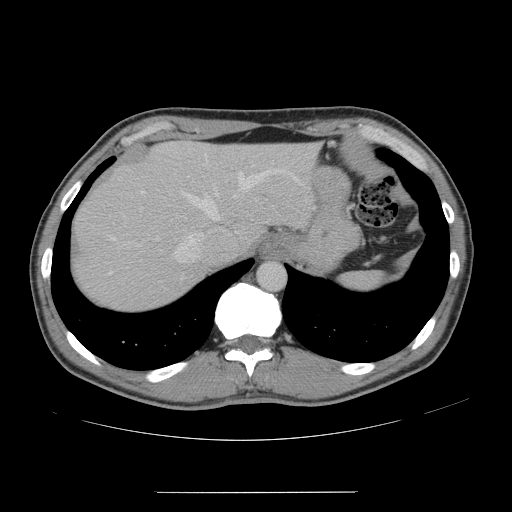
Contrast-enhanced abdominal CT, one axial slice; position 124 of 178 along the scan axis; 120 kVp; intravenous contrast given; soft-tissue window (W 400 / L 40 HU); 2.5 mm slice thickness; 512 × 512 image matrix, field of view 401 × 401 mm. Male patient, age 53 years. From the clinical record (not read from this slice): diagnosis: colorectal cancer liver metastases, imaged before liver resection; multiple liver metastases: yes; largest metastasis: 2.4 cm.
Outlined on this slice (outlined manually by an expert reader):
- hepatic veins: bounding box (x1, y1, x2, y2) in pixels: (110, 169, 298, 262)
- liver: (73, 142, 319, 310)
- planned liver remnant (the part of the liver to remain after resection): (154, 141, 318, 245)